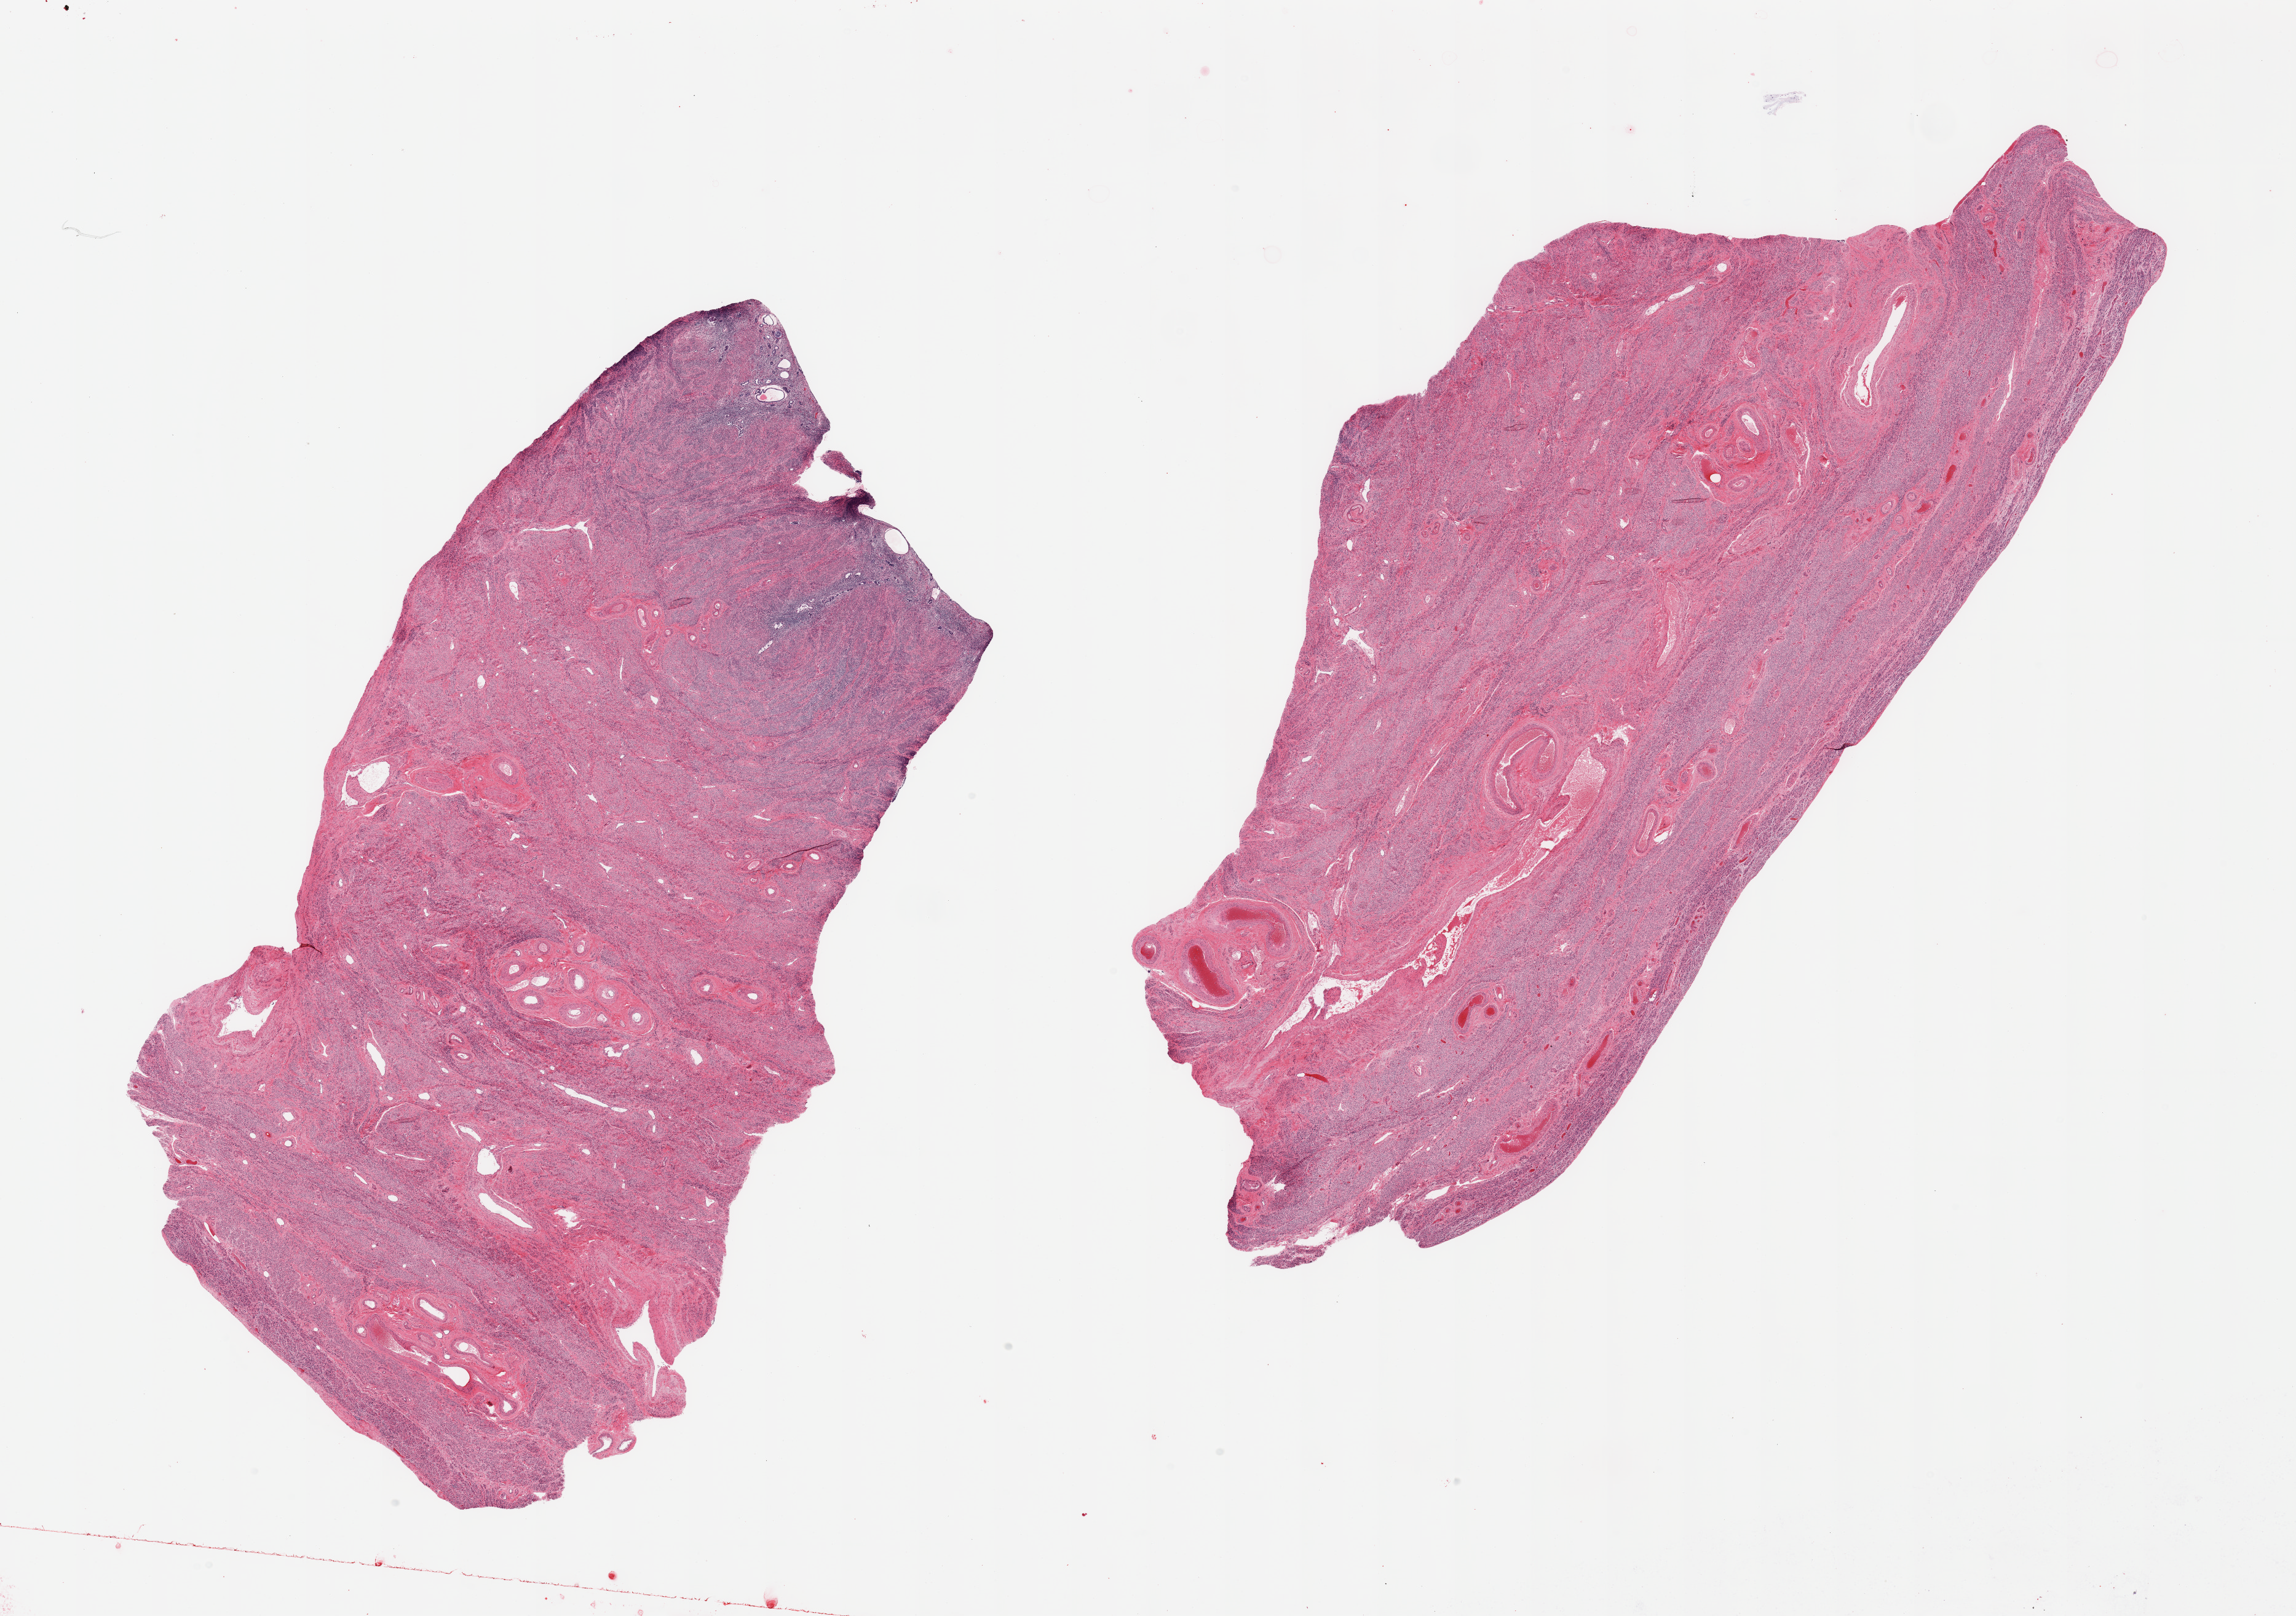
Digitized haematoxylin and eosin-stained section, brightfield — a low-resolution overview of the entire scanned area, about 29.5 x 20.8 mm (acquisition: 20x scan); PAXgene-fixed paraffin-embedded (PFPE) section; section of uterus (target tissue); donor tissue sample. Donor sex: female.
Pathologist's review note for this sample: 2 pieces; atrophic endometrium occupies 20% of 1 piece, 10% of other.